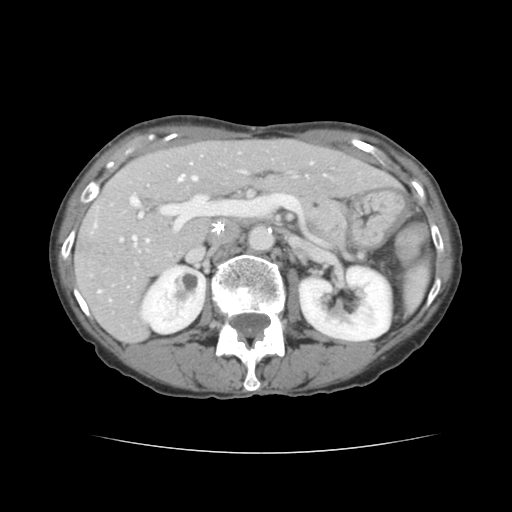
Contrast-enhanced abdominal CT, one axial slice. Slice 75 of 136 in the series (ordered by position). 120 kVp. Intravenous contrast given. Soft-tissue window (W 400 / L 40 HU). 2.5 mm slice thickness. 512 × 512 image matrix. Female patient, age 77 years. From the clinical record (not read from this slice): diagnosis: colorectal cancer liver metastases, imaged before liver resection.
Outlined on this slice (manually delineated by an expert):
- hepatic veins: bounding box (x1, y1, x2, y2) in pixels: (133, 175, 197, 239)
- liver: (75, 140, 392, 341)
- planned liver remnant (the part of the liver to remain after resection): (156, 140, 392, 199)
- portal vein (with intrahepatic branches): (95, 171, 246, 293)